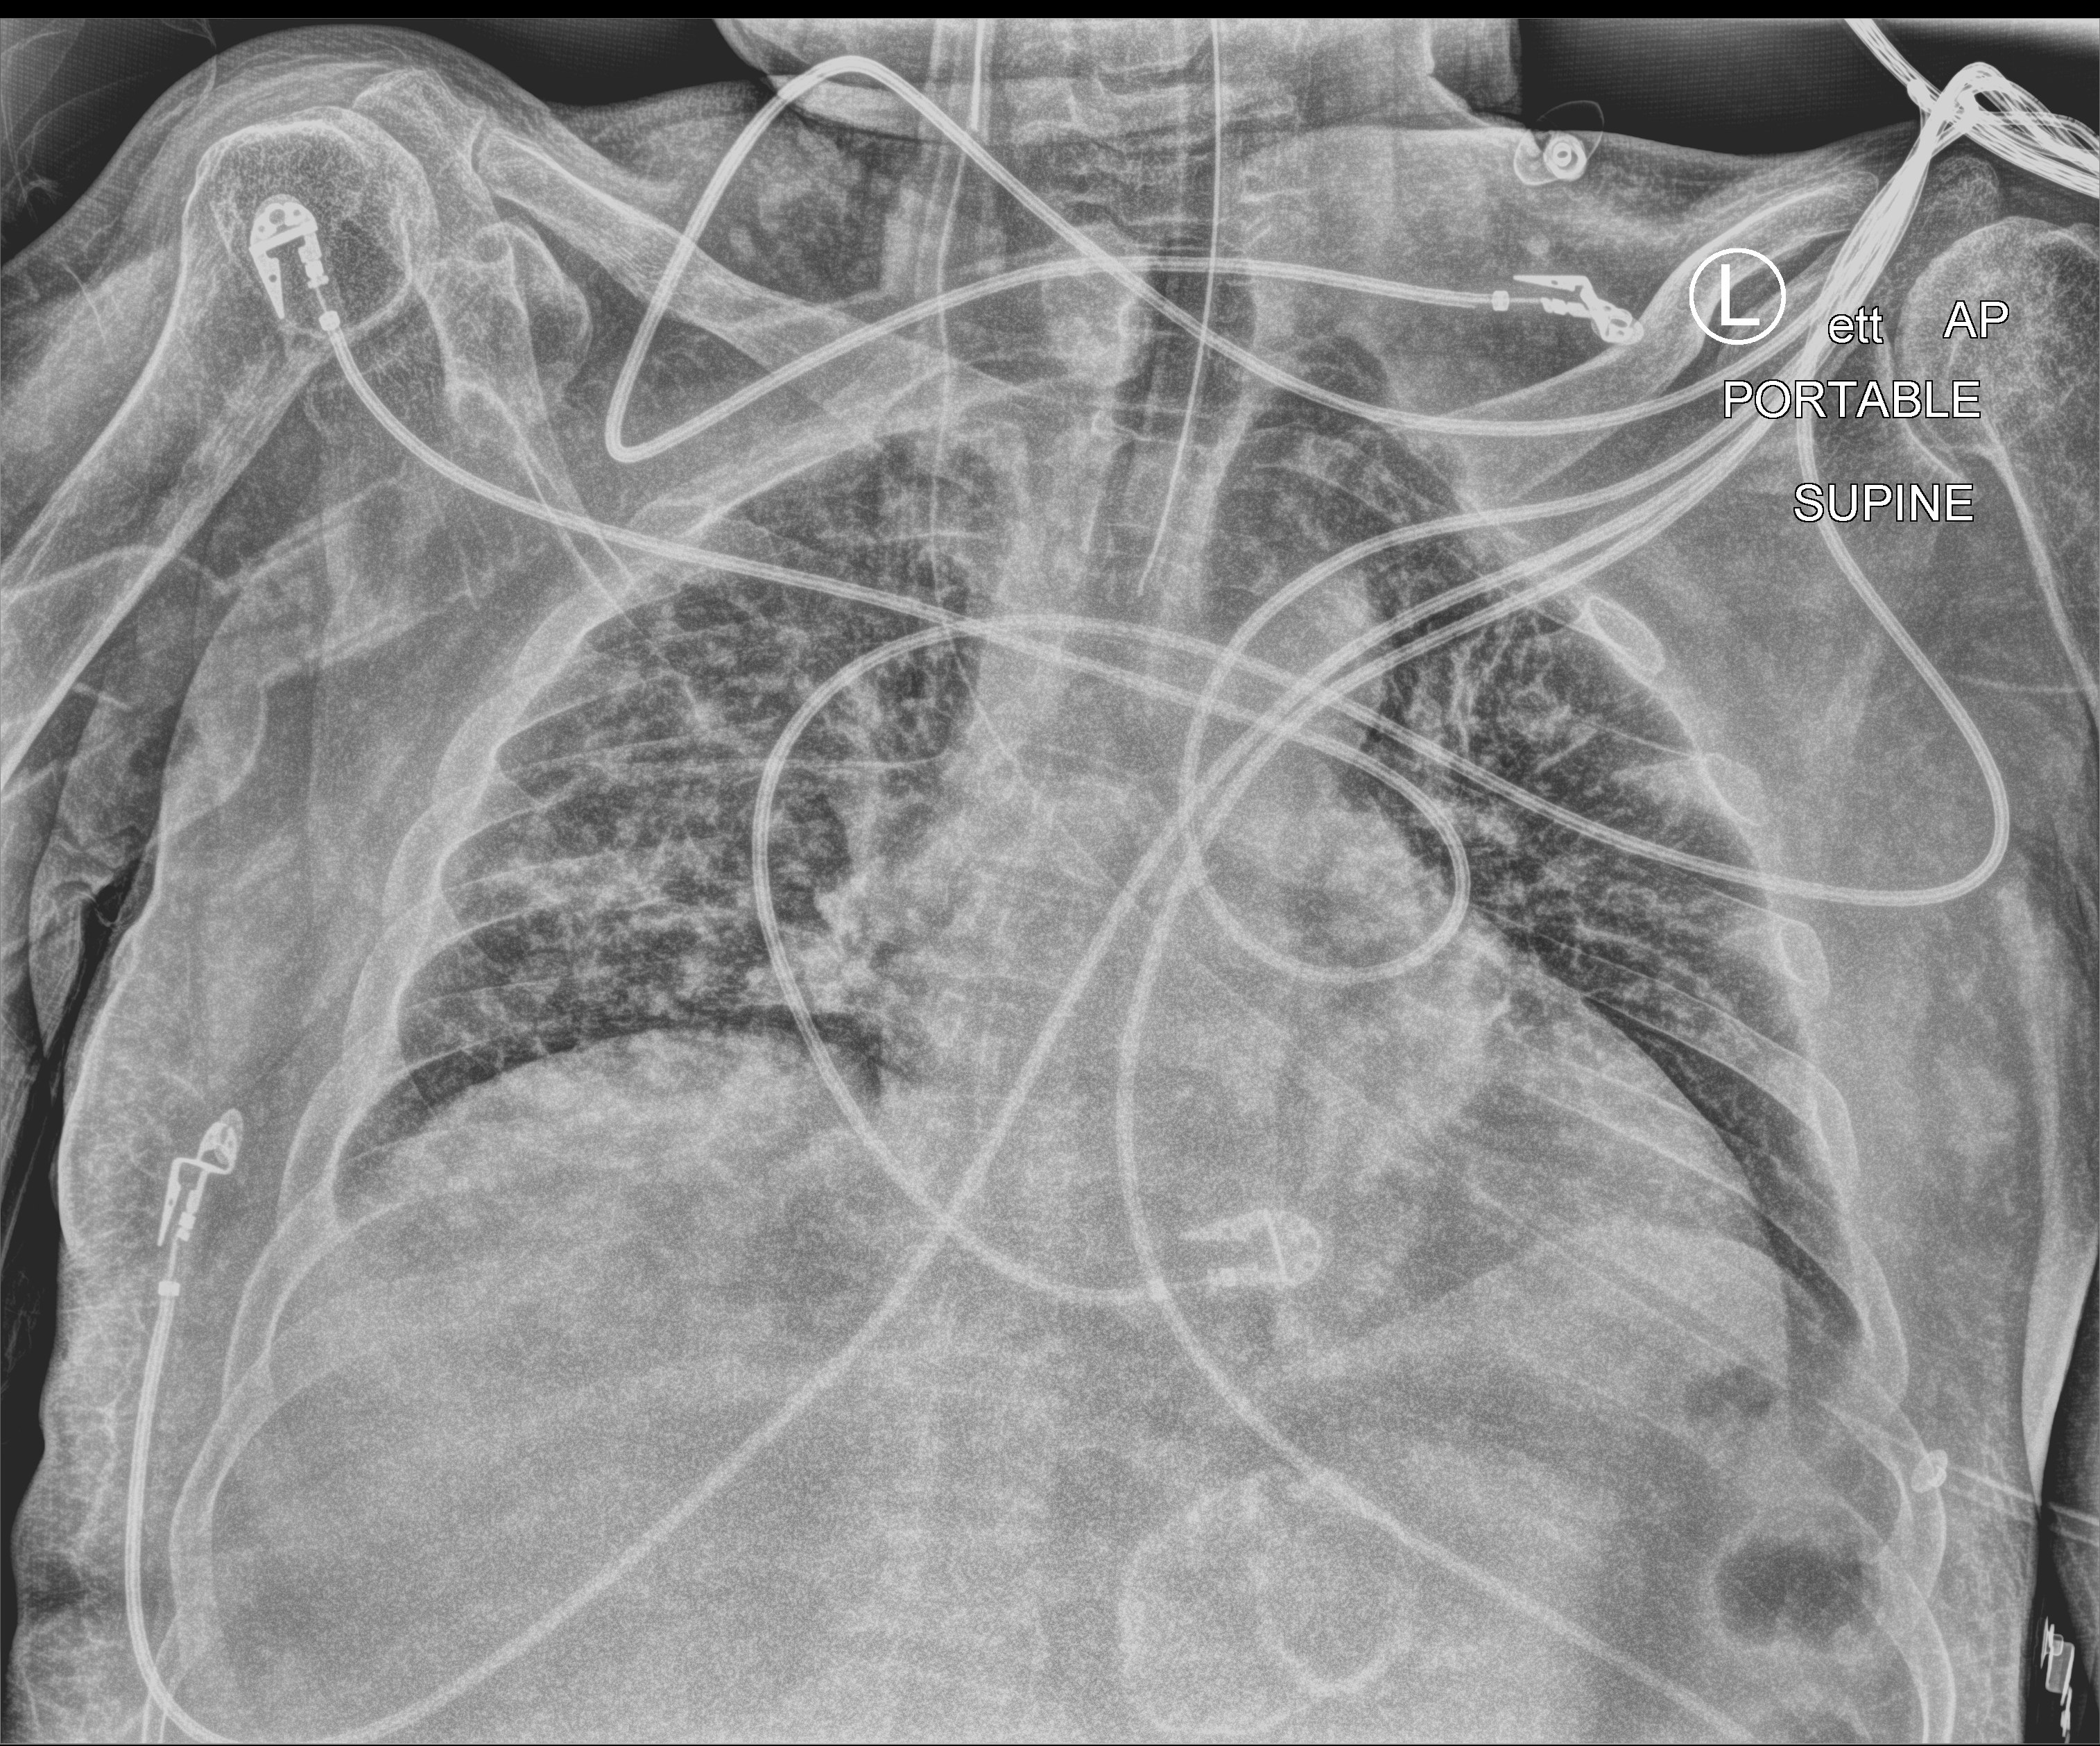
Portable chest radiograph; anteroposterior (AP) projection. Male patient hospitalised with COVID-19, age 60–74 years.
Admission-level facts for this patient (not findings on this image; timing relative to this image not recorded): admitted to intensive care during this hospital stay: yes; length of hospital stay: 4 days; hypertension (admission record): no.